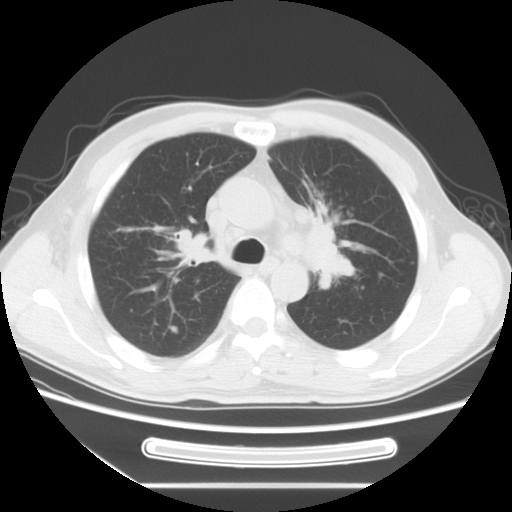
Chest CT, one axial slice; slice 49 of 71 in the series (ordered by position); reconstruction kernel STANDARD; 120 kVp; lung window (W 1500 / L -600 HU); 5 mm slice thickness; 512 × 512 image matrix. Patient: male, 51 years. Case-level facts recorded for this patient, not image findings: clinical TNM (as recorded): T1c N3 M0.
Structures marked on this image (rectangle marked by the reading radiologist):
- lung tumour (recorded histology: adenocarcinoma): box from (x=298, y=199) to (x=363, y=306) px